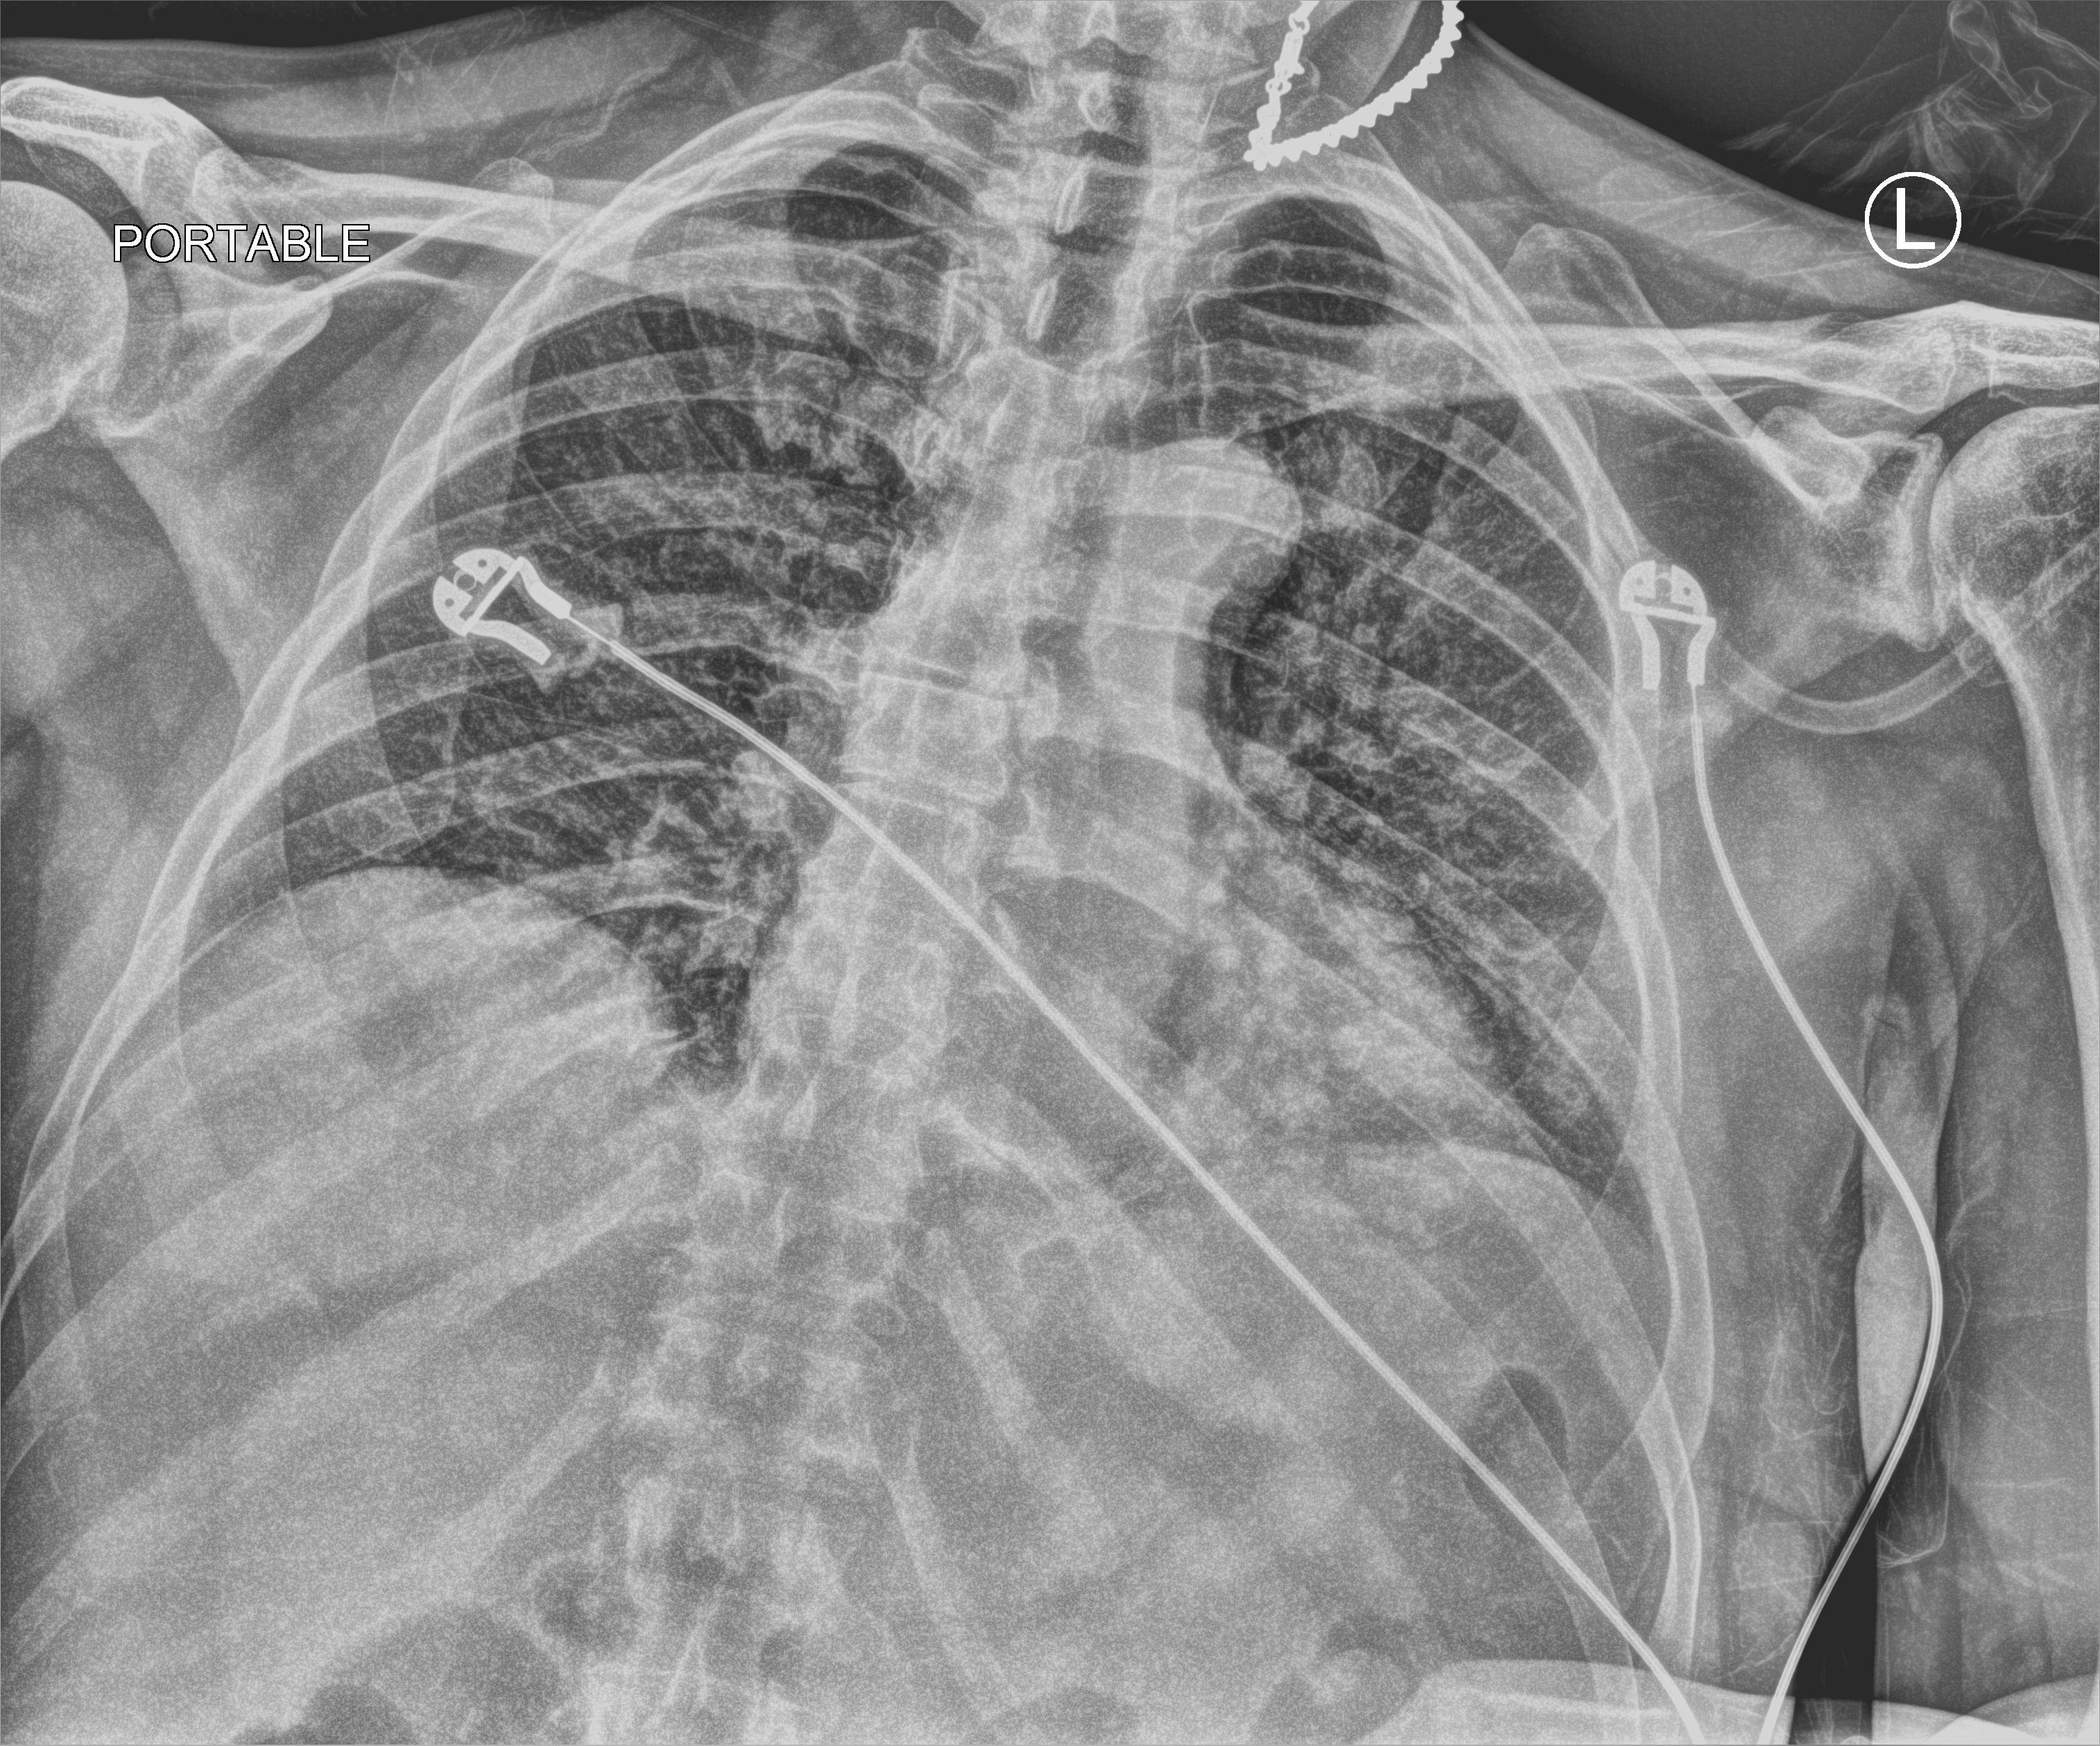
Chest X-ray (portable); anteroposterior (AP) projection. Male patient hospitalised with COVID-19, age 60–74 years.
From the hospital-stay record, not from the radiograph (when in the stay this image was taken is not recorded):
- admitted to intensive care during this hospital stay: no
- mechanically ventilated during this hospital stay: no